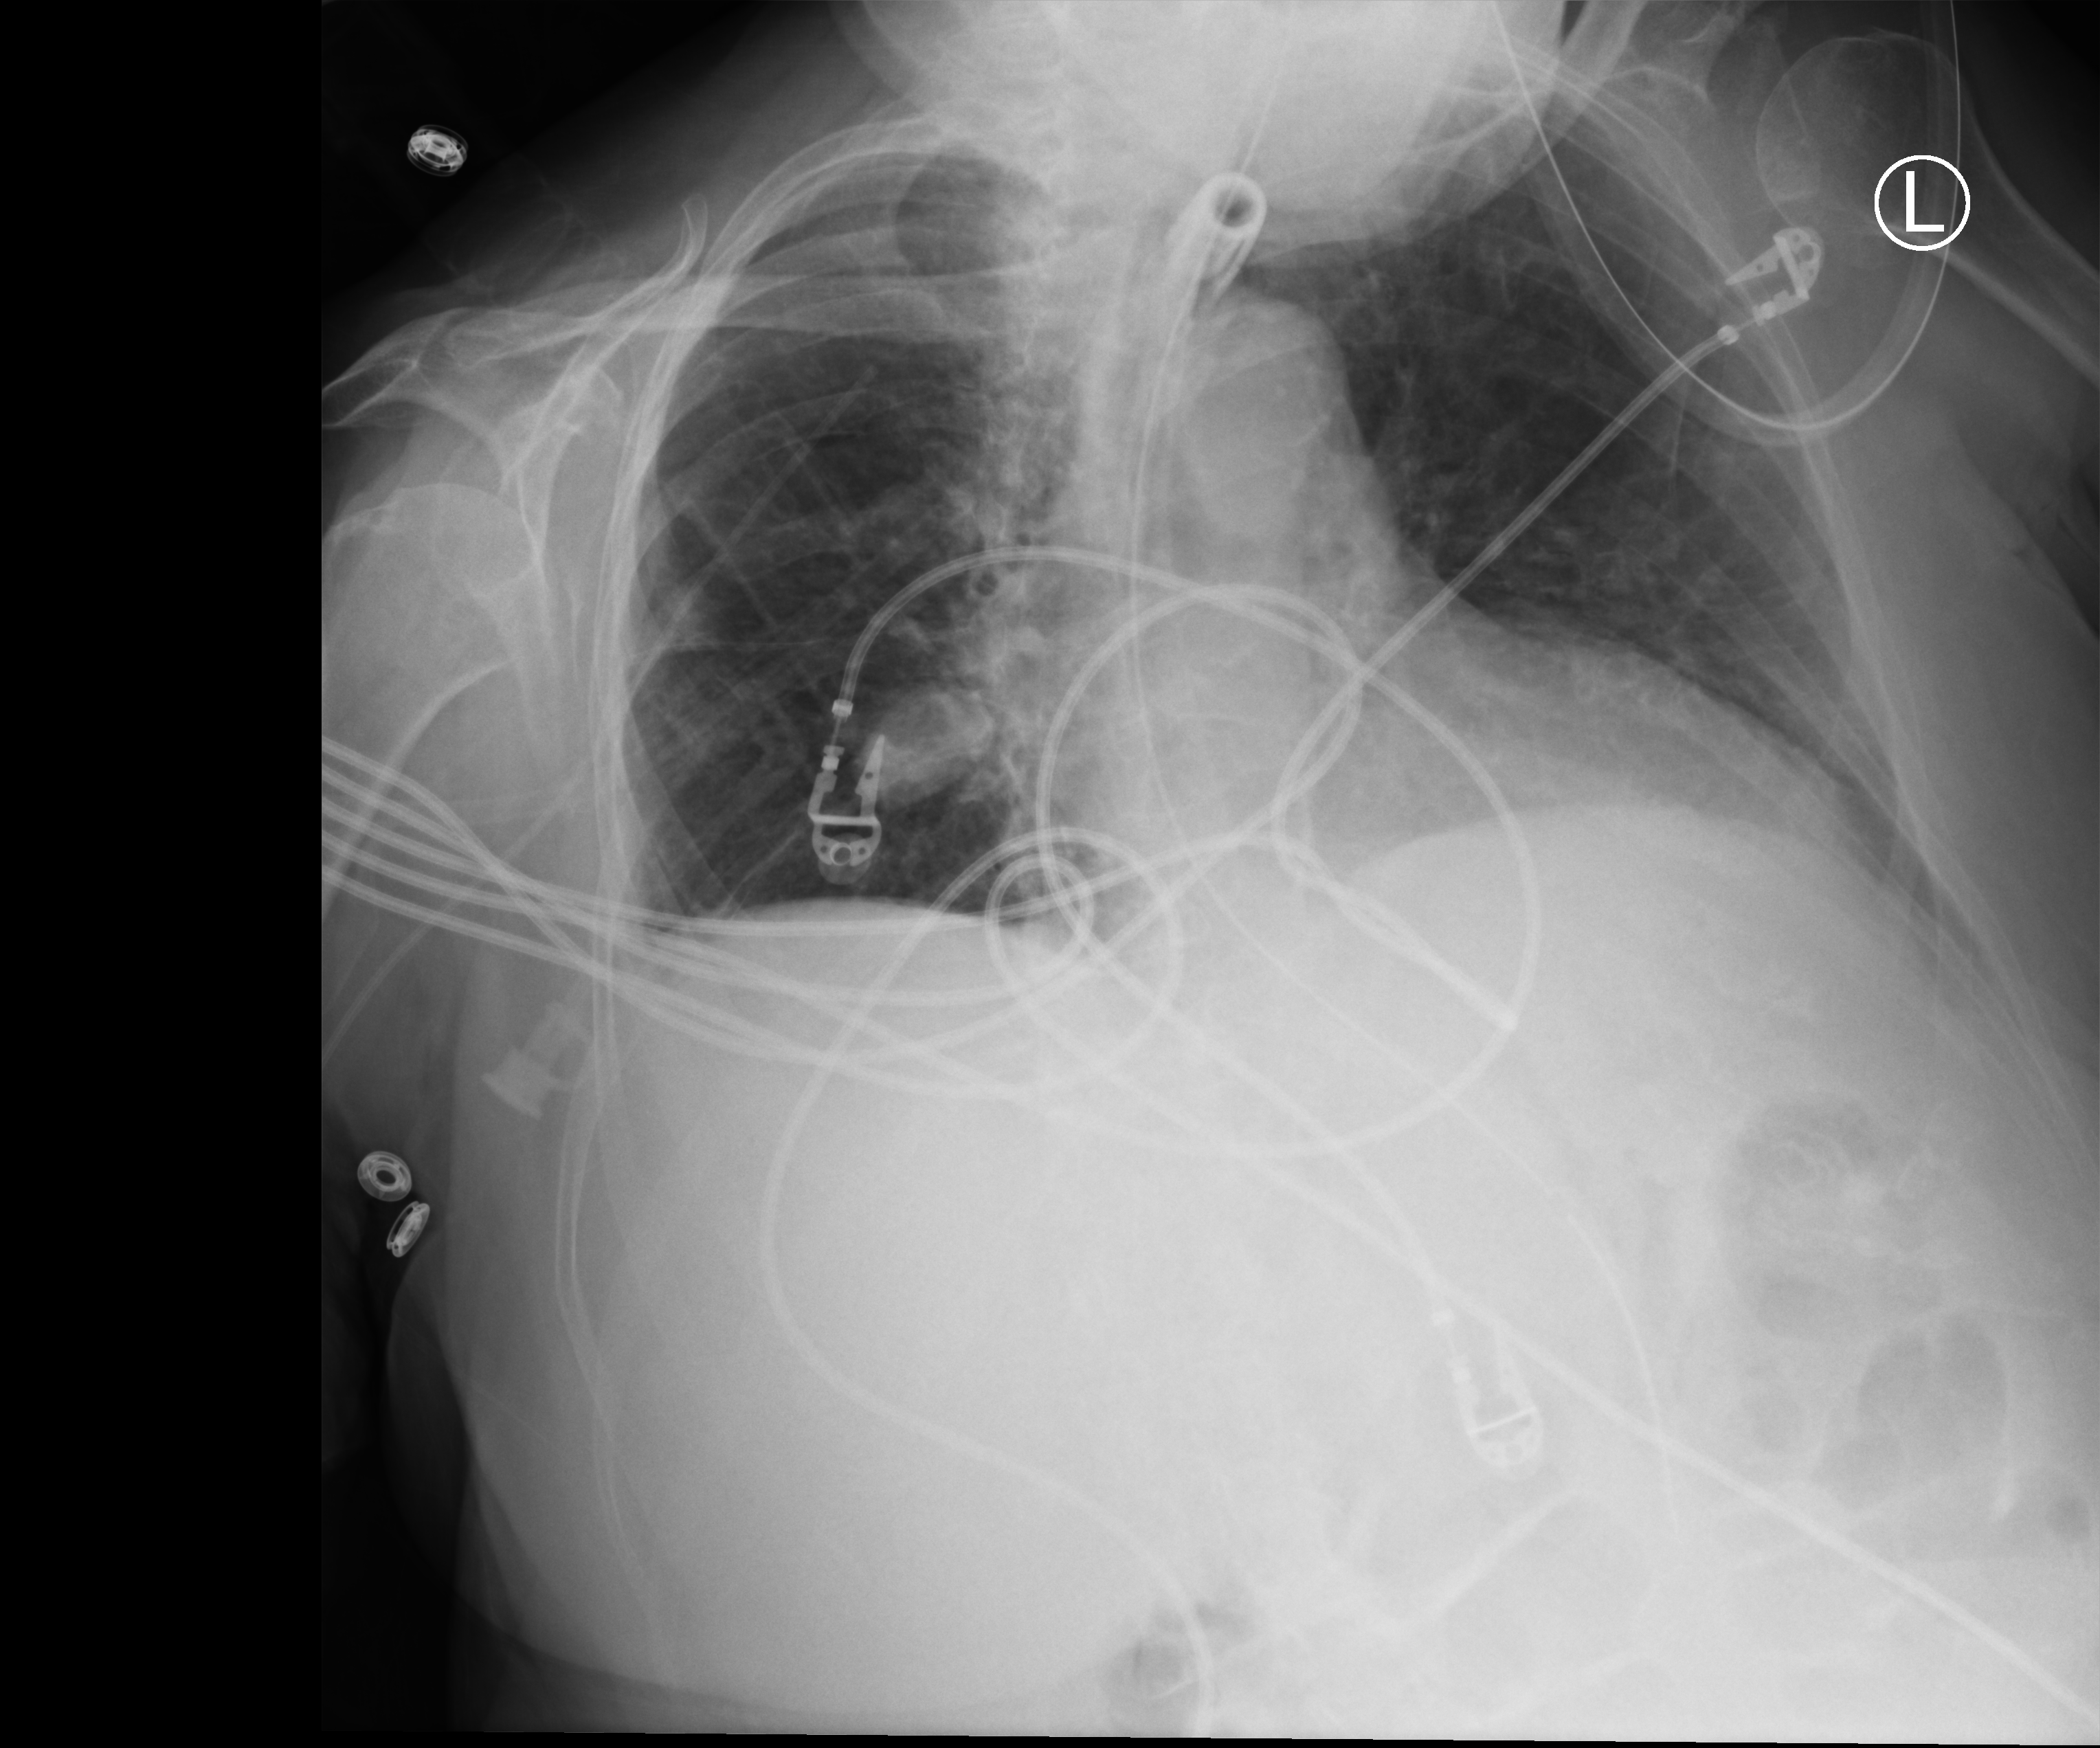
Chest X-ray (portable), anteroposterior (AP) projection. Female patient hospitalised with COVID-19, age 75–90 years.
Hospital-stay facts (about this admission, not read from this image; timing relative to this image not recorded): mechanically ventilated during this hospital stay: yes; admitted to intensive care during this hospital stay: yes; length of hospital stay: 82 days.